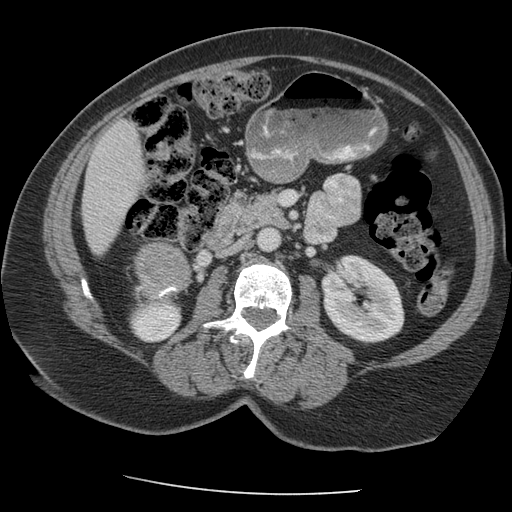
Contrast-enhanced abdominal CT, one axial slice. Position 105 of 163 along the scan axis. Reconstruction kernel STANDARD. Soft-tissue window (W 400 / L 40 HU). 512 × 512 image matrix. Patient: female, 70 years. From the clinical record (not read from this slice): diagnosis: adrenocortical carcinoma; tumour side: right adrenal; tumour size at pathology: 9.5 cm.
Annotated regions visible in this slice (semi-automatic segmentation, software-assisted and operator-edited):
- mass: box from (x=138, y=243) to (x=190, y=298) px